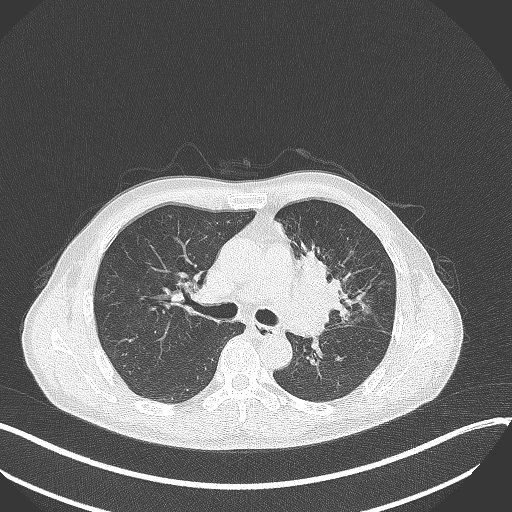
Chest CT, one axial slice. Position 207 of 411 along the scan axis. Reconstruction kernel B70f. 120 kVp. Lung window (W 1500 / L -600 HU). 512 × 512 image matrix. Patient: male, 56 years. Case-level facts recorded for this patient, not image findings: clinical TNM (as recorded): T2a N0 M0.
Annotated regions visible in this slice (bounding box drawn by a radiologist):
- lung tumour (recorded histology: squamous cell carcinoma): bounding box [x1, y1, x2, y2] px = [290, 244, 352, 325]